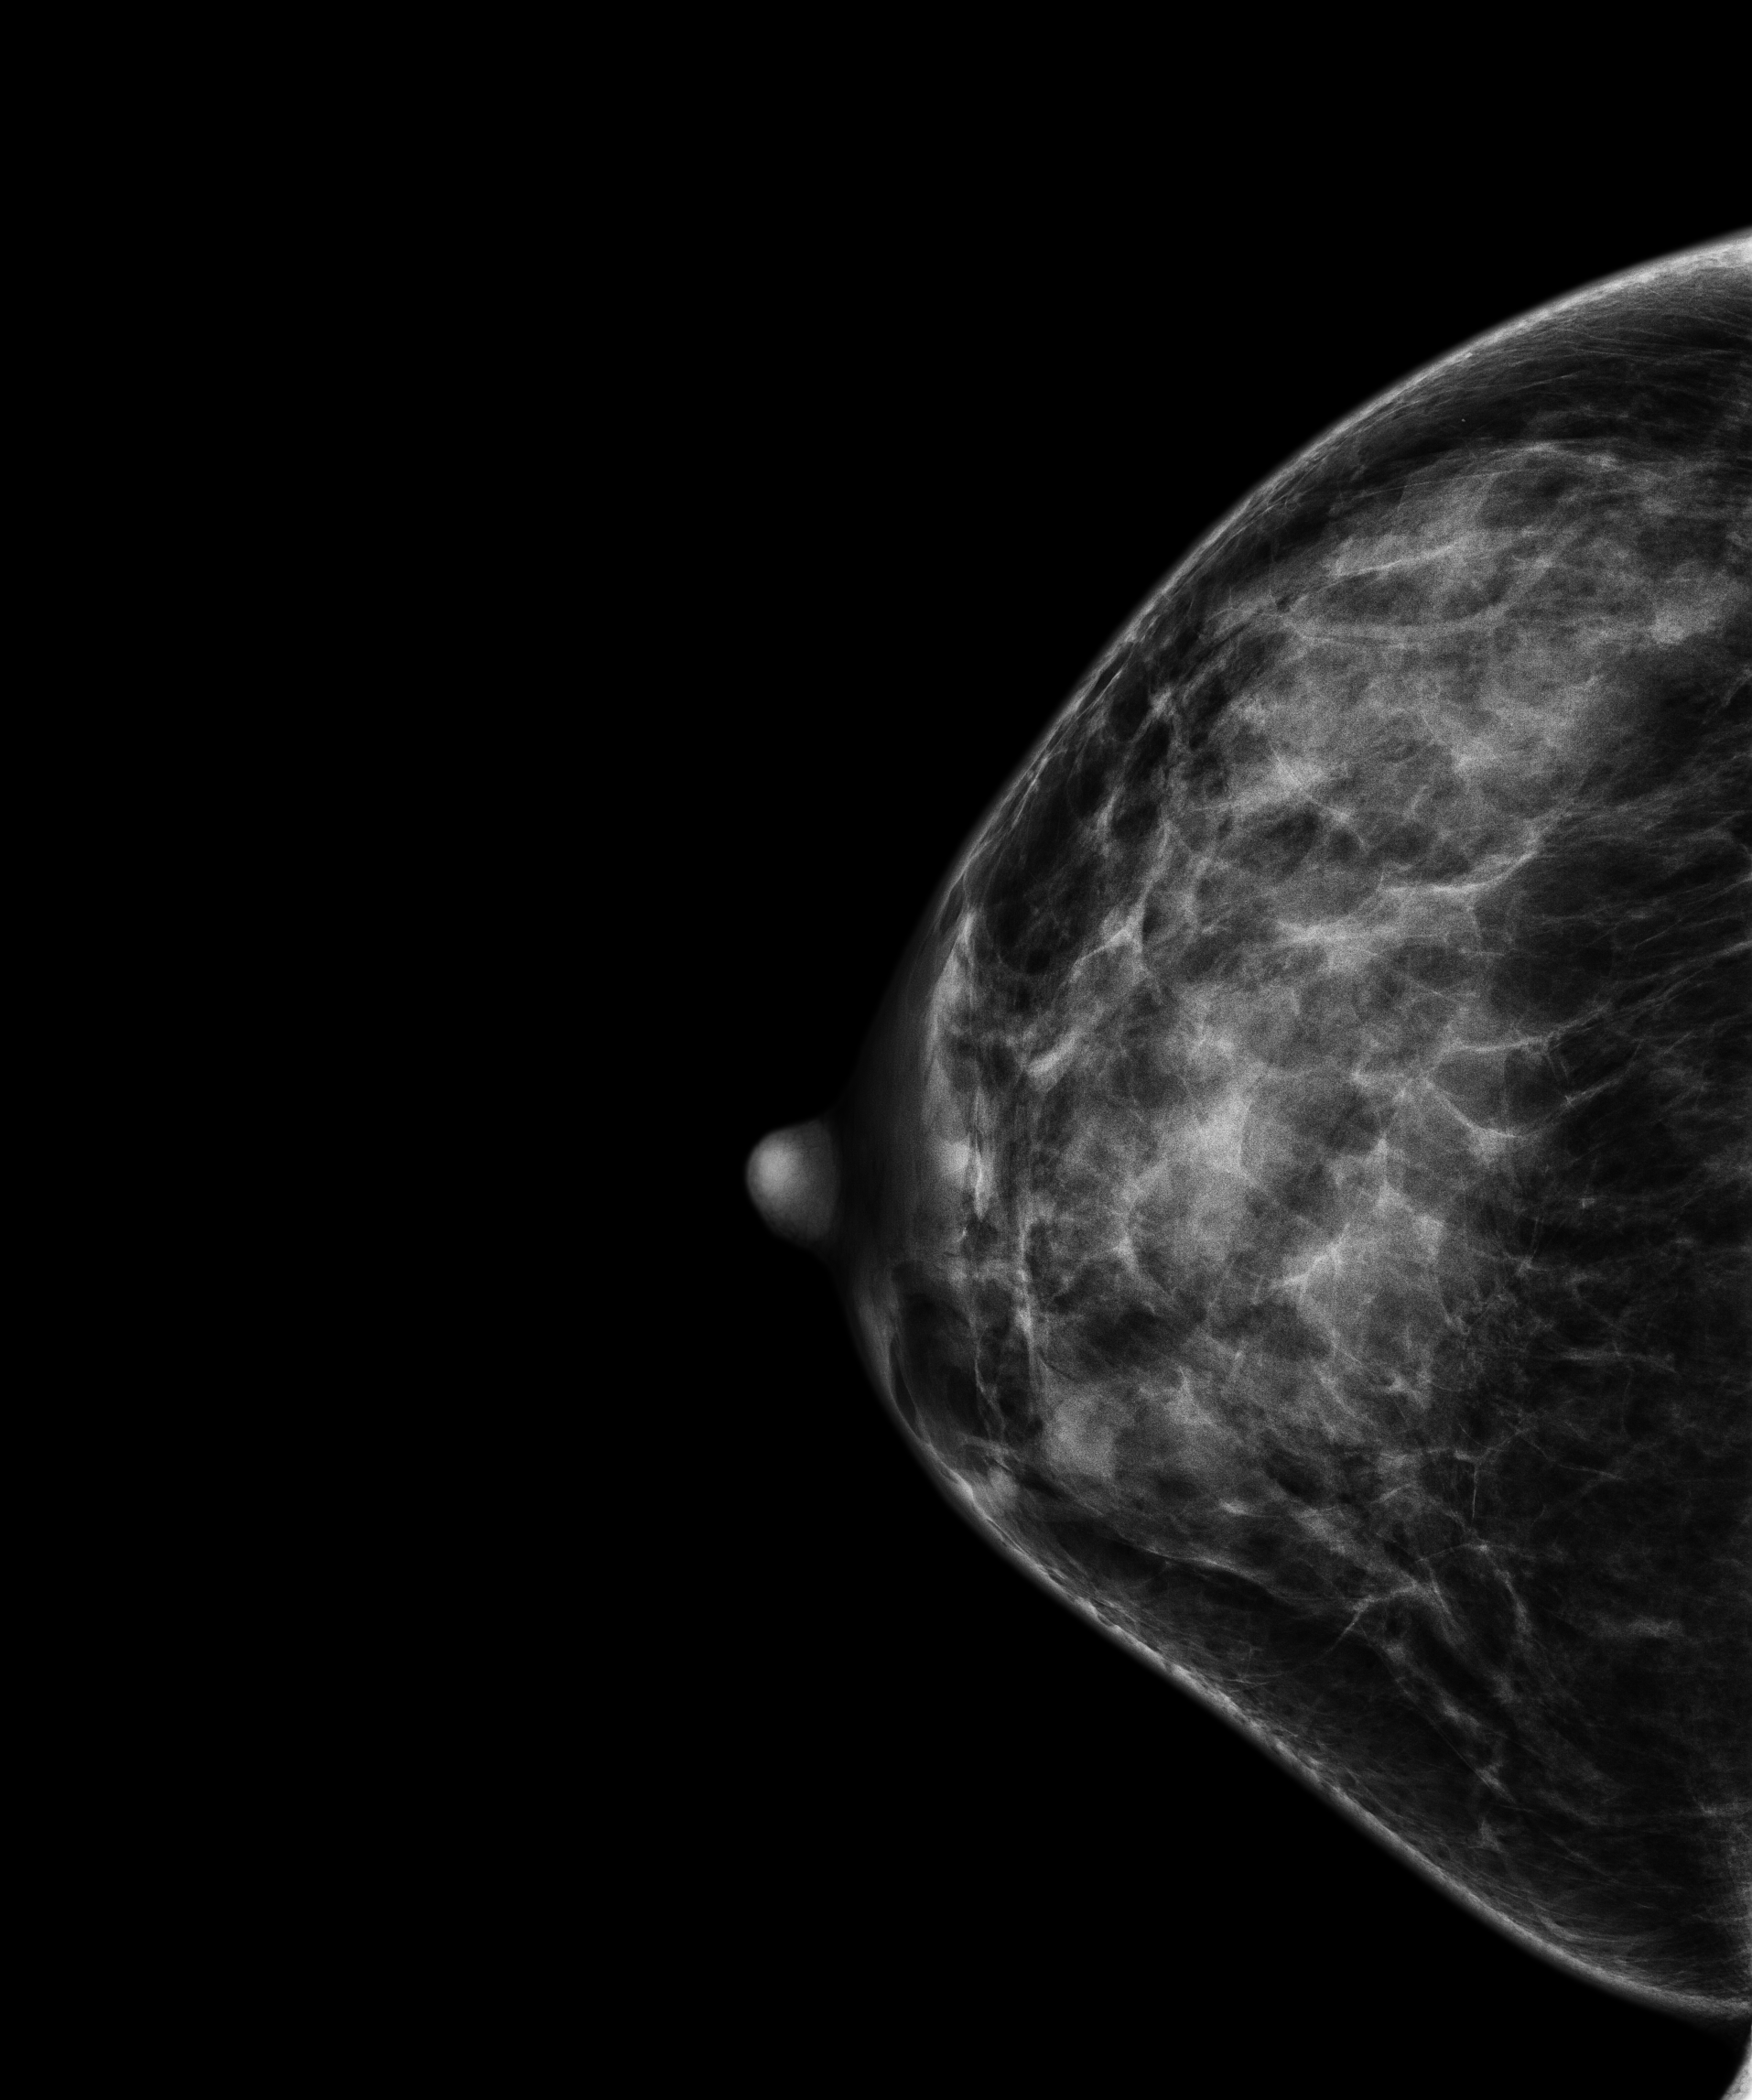
Annual screening mammography examination, compressed breast thickness 44 mm. Patient: female, 56 years.
Image type: full-field digital mammogram. Breast: right. Projection: craniocaudal (CC) view.